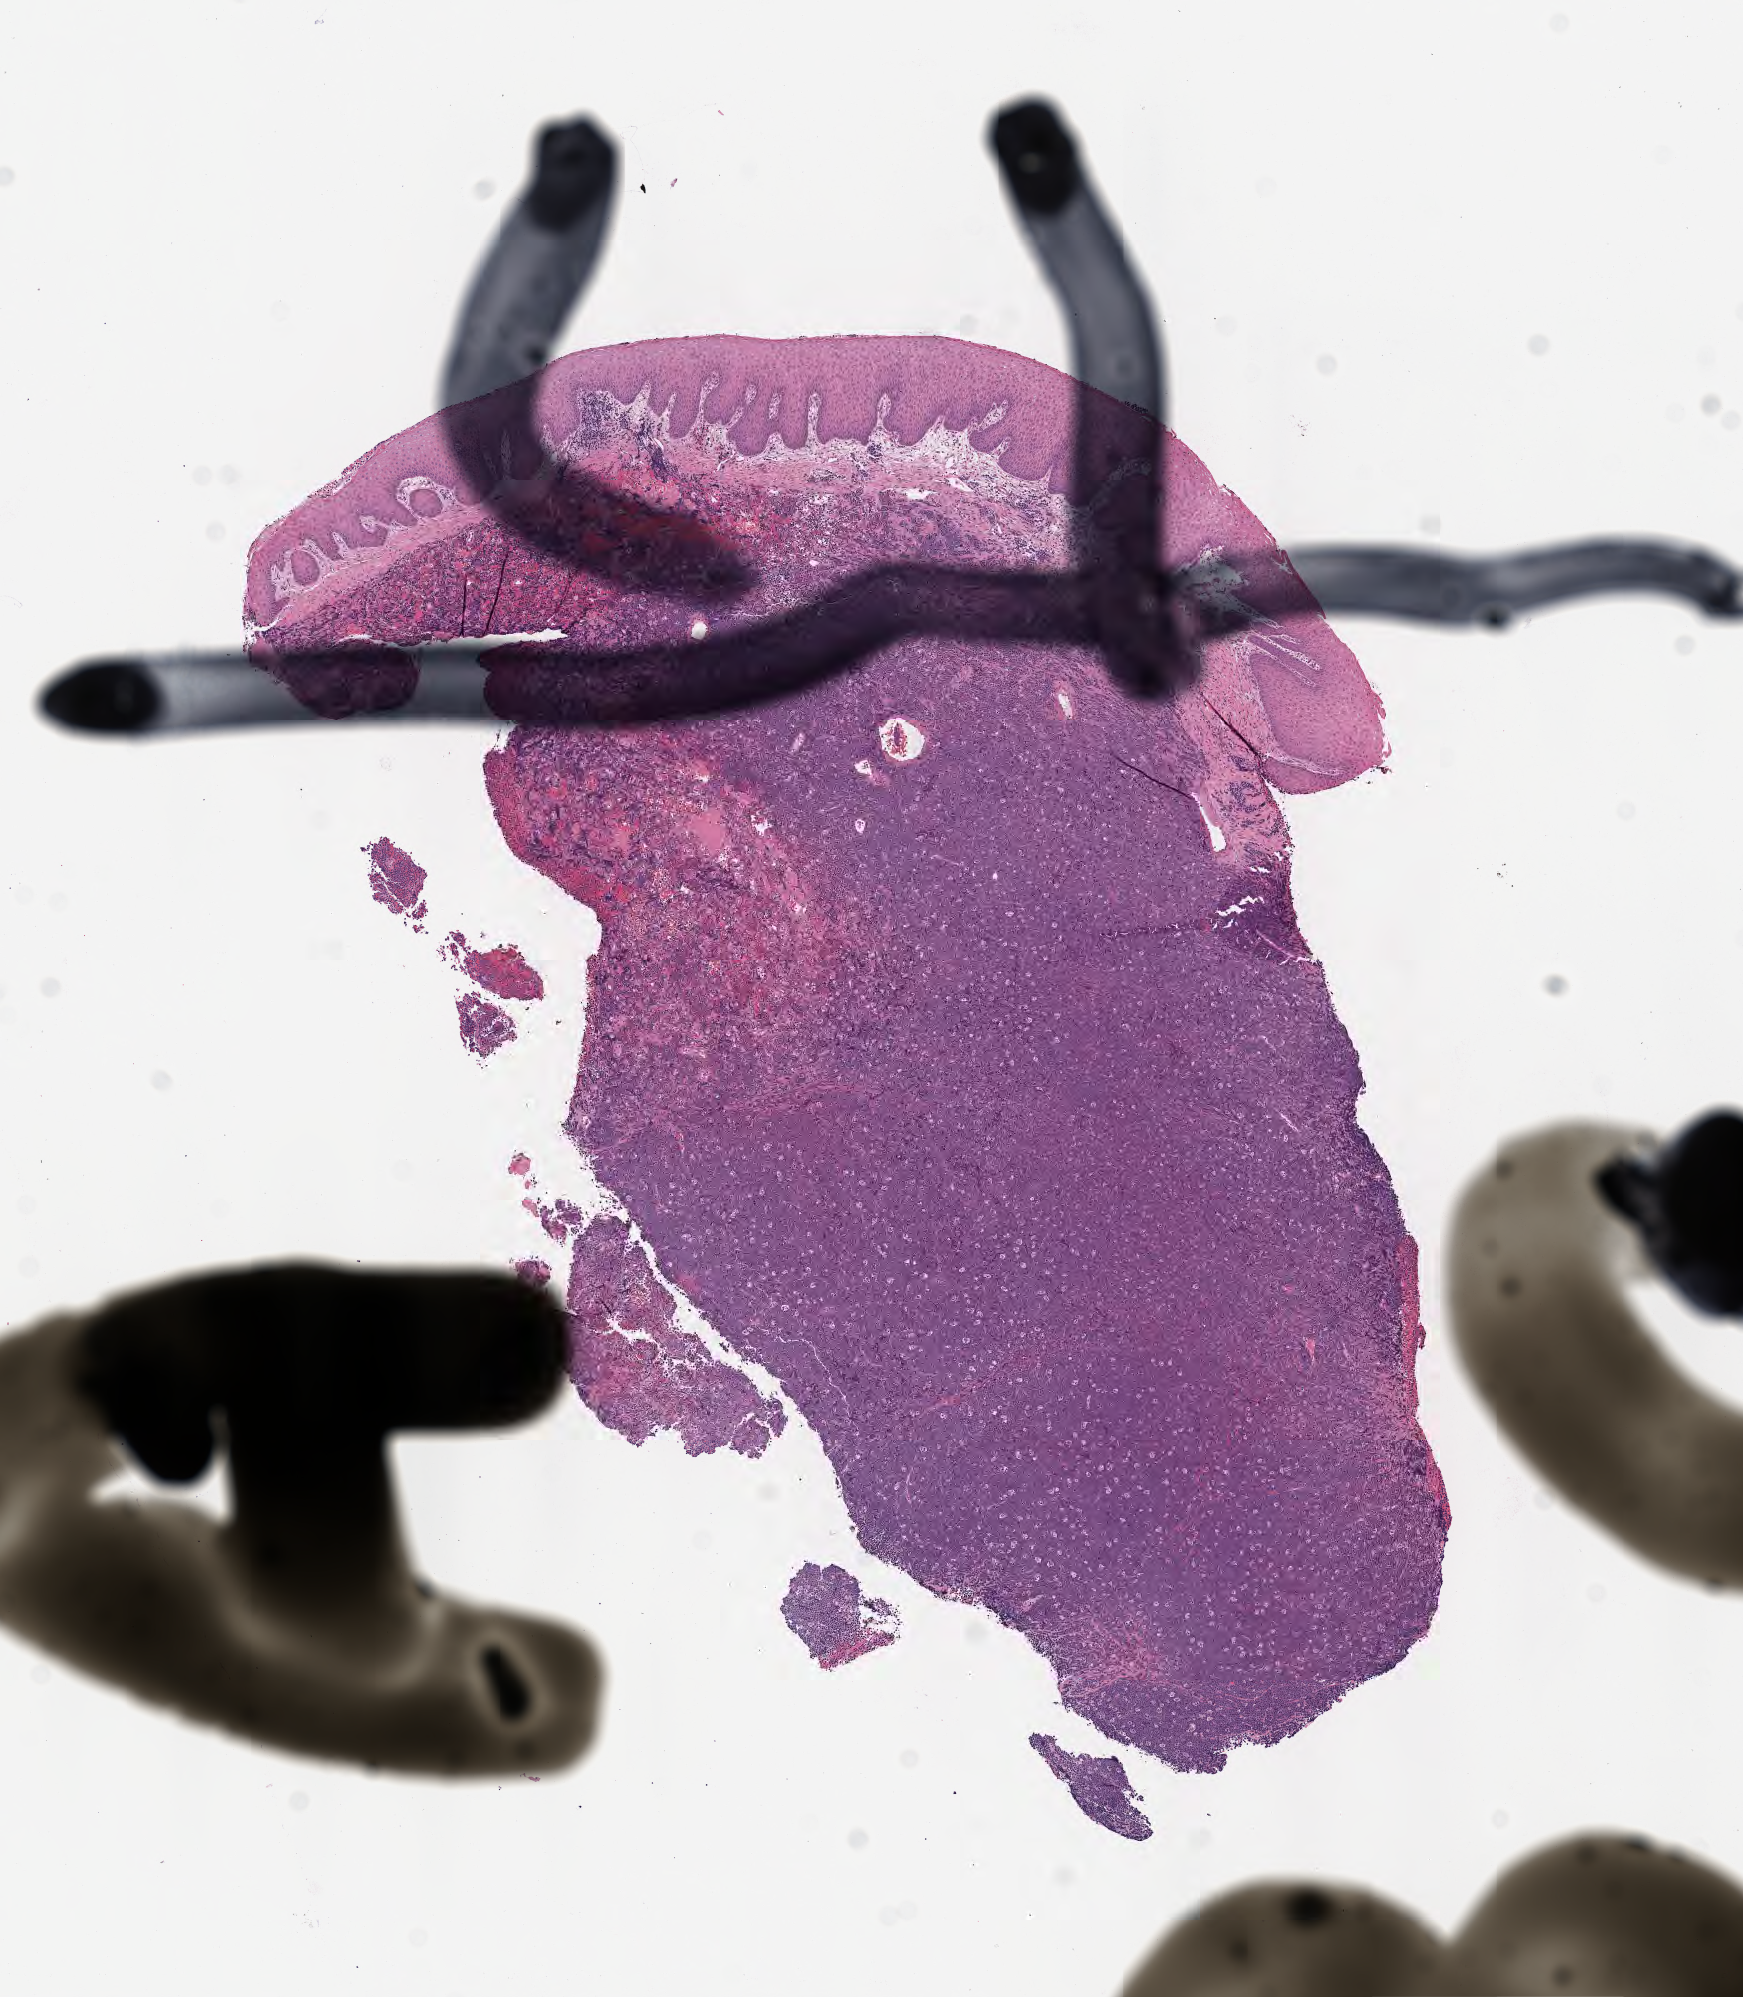
Digitized hematoxylin and eosin (H&E)-stained section, low-resolution overview of the scanned area, about 7.0 x 8.1 mm. Tumor tissue. Site: cranium. Patient: female, age at initial diagnosis 3 years.
Histologic diagnosis: Burkitt lymphoma, NOS.